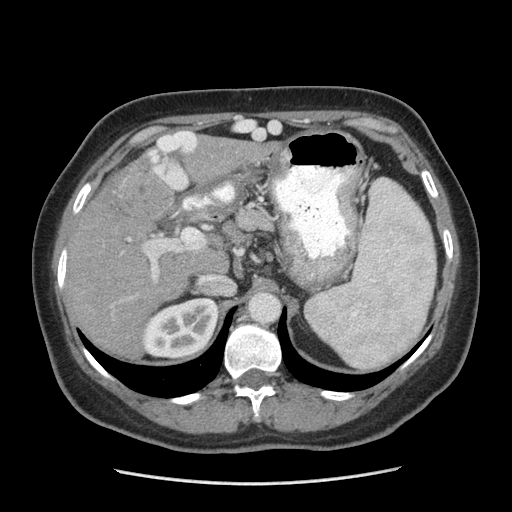
Contrast-enhanced abdominal CT (liver protocol), one axial slice. Slice 154 of 185 in the series (ordered by position). Reconstruction kernel STANDARD. Soft-tissue window (W 400 / L 40 HU). 2.5 mm slice thickness. 512 × 512 image matrix, field of view 360 × 360 mm. From the clinical record (not read from this slice): diagnosis: hepatocellular carcinoma (patient treated with transarterial chemoembolisation; whether this scan precedes or follows treatment is not stated here); TNM stage (as recorded): Stage-I; Child-Pugh class: A; tumour differentiation: poorly differentiated.
Structures marked on this image (semi-automatically segmented with operator editing):
- liver parenchyma outside the tumour (the mass and vessels are separate outlines, so this box may not span the whole liver): box from (x=64, y=136) to (x=245, y=356) px
- mass: (x=110, y=163)–(x=171, y=222)
- liver vessels: (x=128, y=150)–(x=210, y=279)